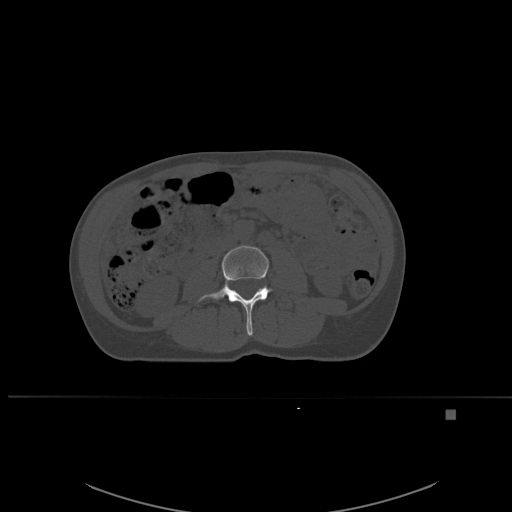
CT including the spine, one axial slice; slice 212 of 537 in the series (ordered by position); bone window (W 1800 / L 400 HU); 512 × 512 image matrix, field of view 440 × 440 mm. Female patient, age 45 years. From the clinical record (not read from this slice): primary cancer: lung.
Outlined on this slice (semi-automatic segmentation, software-assisted and operator-edited):
- L3 vertebra: bounding box <198,245,273,336> (left, top, right, bottom; pixels)